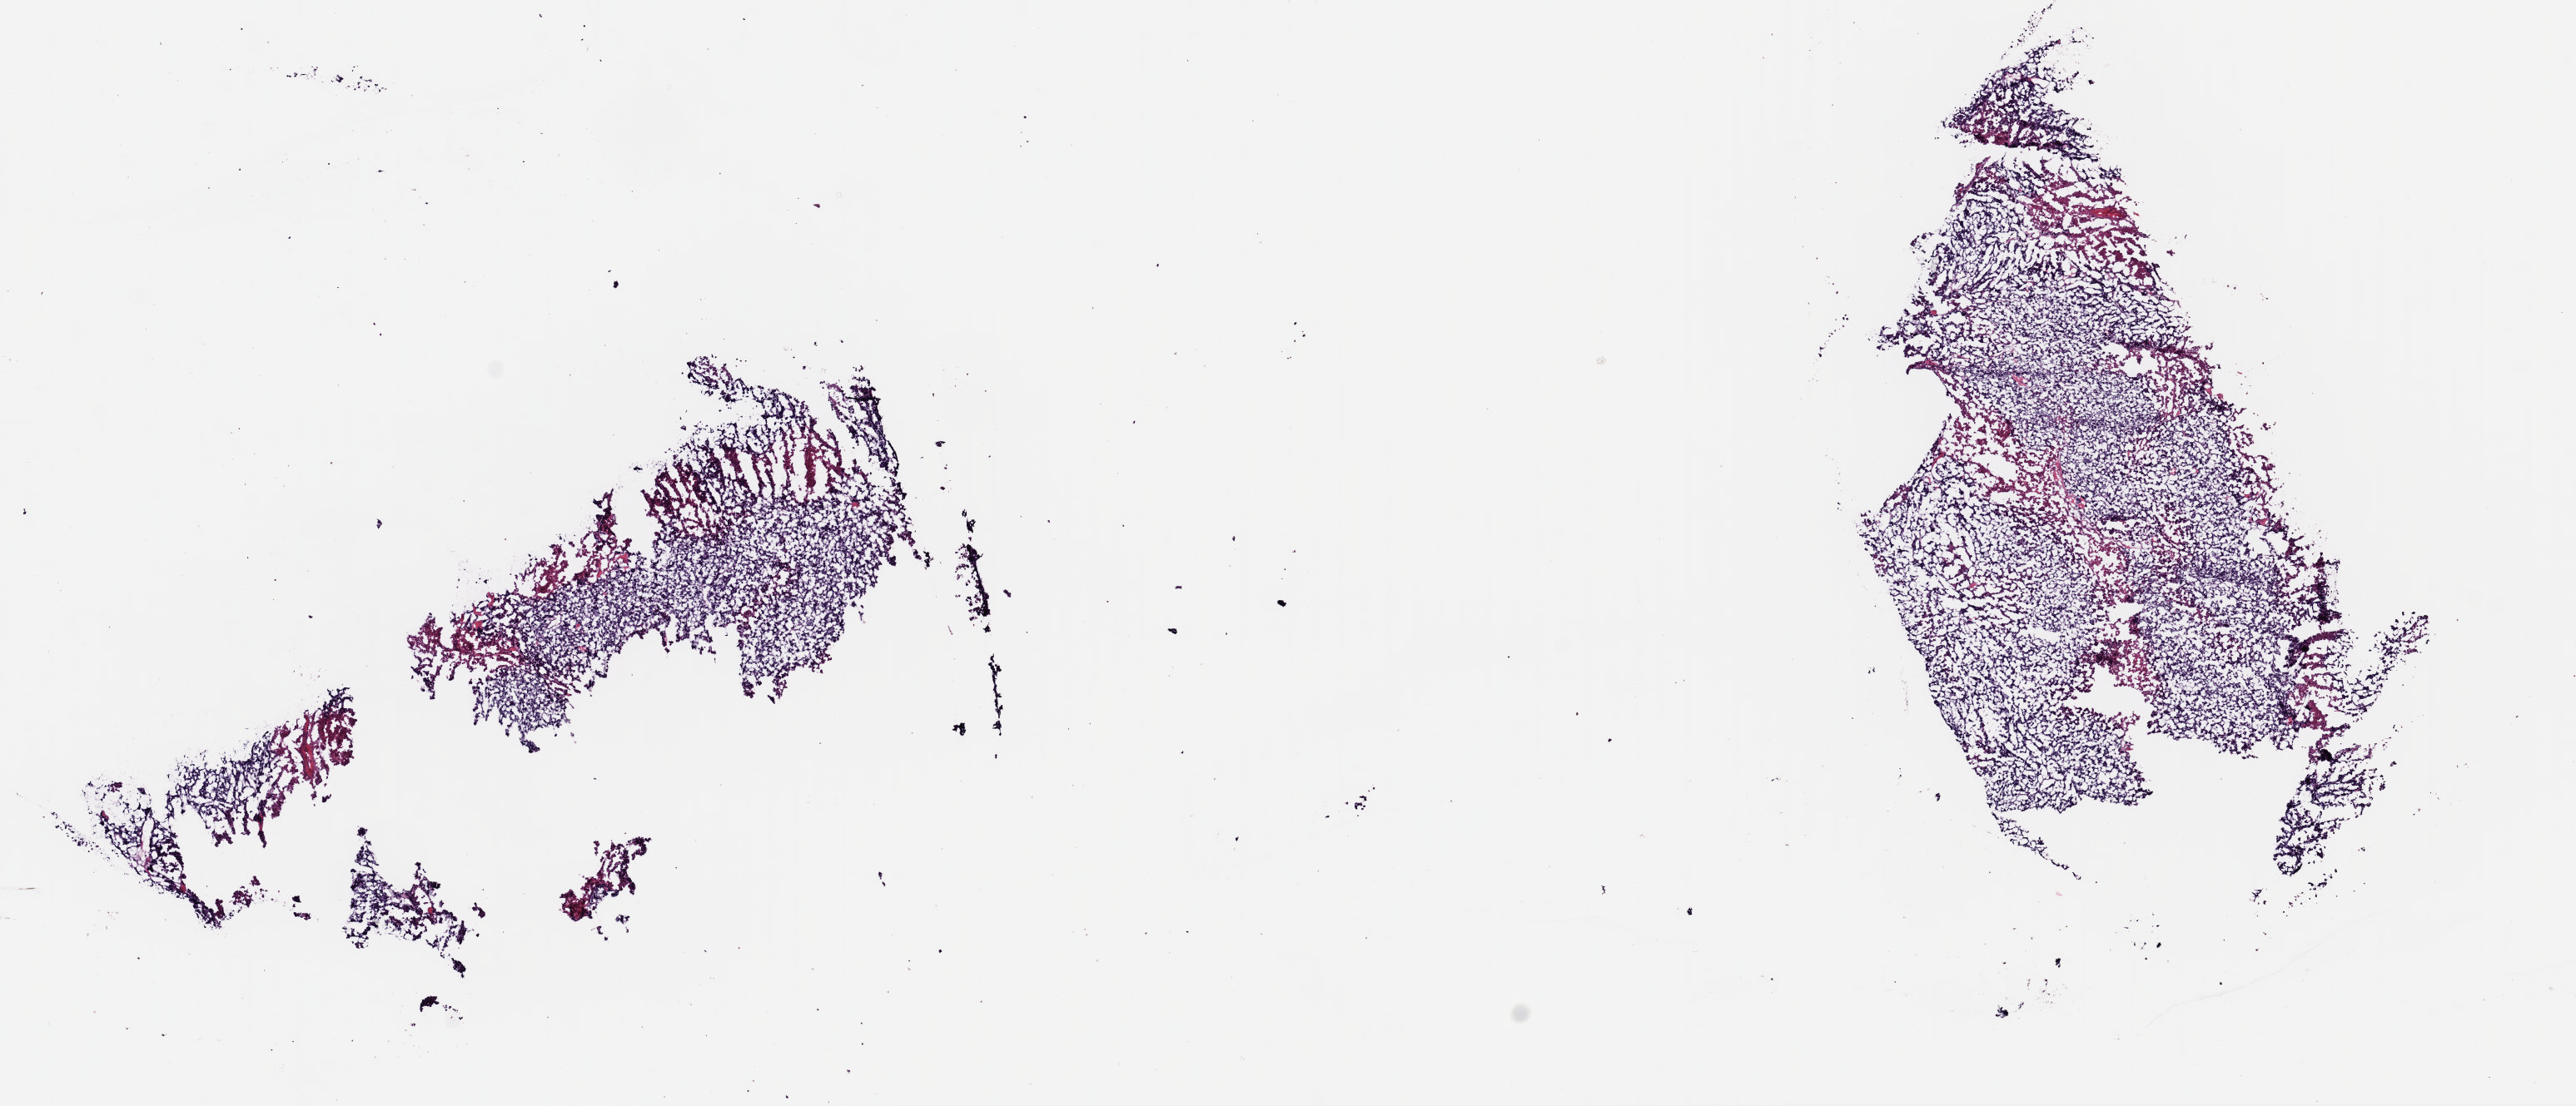
Digitized H&E tissue section (whole slide), a low-resolution overview of the entire scanned area, about 12.2 x 5.2 mm (from a 40x scan), frozen section from the top of the tissue portion, metastatic tumour sample, sampled site not recorded. Male, age 56 years at initial diagnosis. Composition of this section per pathologist review: tumour cells 90%, tumour nuclei 95%, normal cells 0%, stromal cells 0%, necrosis 10%. Infiltration values recorded for this section: lymphocyte infiltration 0%, monocyte infiltration 0%, neutrophil infiltration 0%.
• this section: metastatic tumour tissue
• patient diagnosis: Malignant melanoma, NOS